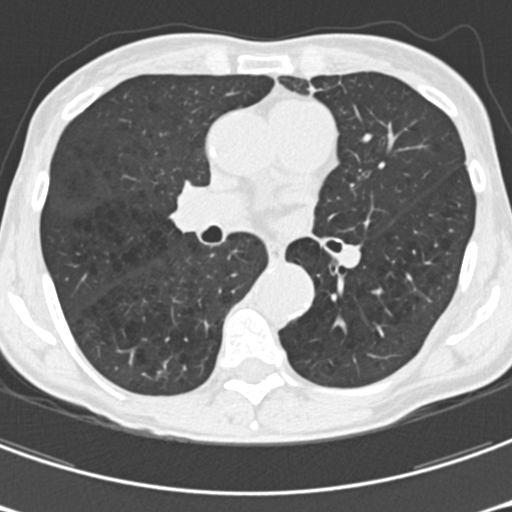
Low-dose screening chest CT, one axial slice. Position 97 of 176 along the scan axis. Reconstruction kernel B30f. Lung window (W 1500 / L -600 HU). 2 mm slice thickness. 512 × 512 image matrix, field of view 277 × 277 mm.
Annotated regions visible in this slice (expert manual segmentation):
- lesion 2 (nodule, upper lobe of right lung): bounding box <157,370,166,379> (left, top, right, bottom; pixels)